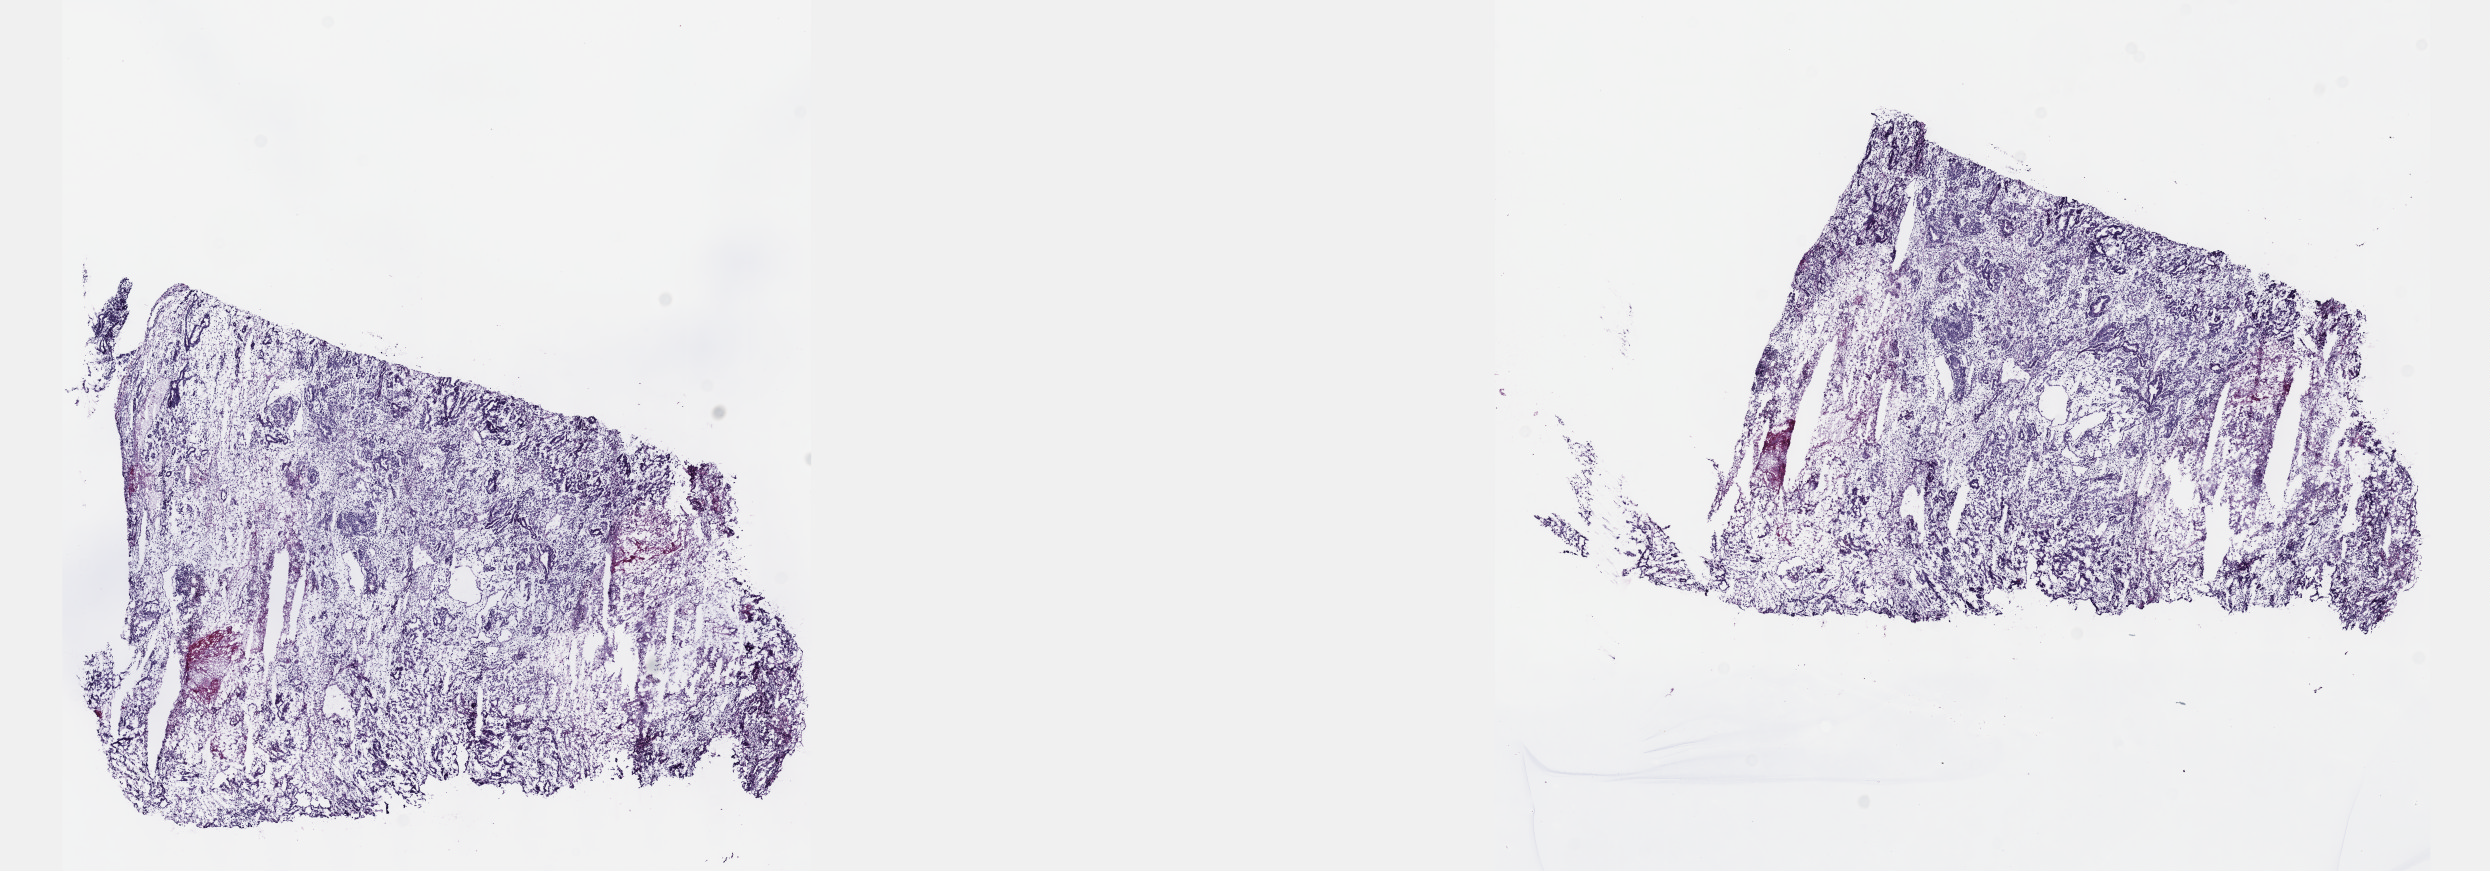
H&E whole-slide image, shown as a low-resolution overview of the whole scanned area (about 20.1 x 7.0 mm). Male patient. Composition of this section per pathologist review: tumour cells 90%, tumour nuclei 90%, normal cells 0%, stromal cells 5%, necrosis 5%. Inflammatory infiltration, as recorded: lymphocyte infiltration 40%, monocyte infiltration 20%, neutrophil infiltration 20%.
• specimen: frozen section; sample: primary tumour, testis